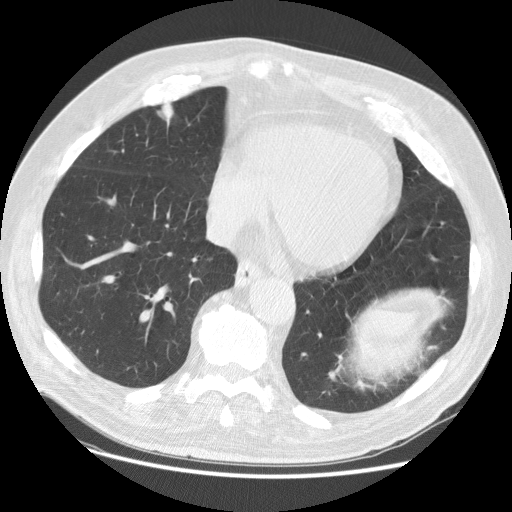
Low-dose screening chest CT, one axial slice. Position 38 of 129 along the scan axis. 140 kVp. Lung window (W 1500 / L -600 HU). 2.5 mm slice thickness. 512 × 512 image matrix, field of view 397 × 397 mm.
Structures marked on this image (expert manual segmentation):
- lesion 1 (tumor, upper lobe of right lung): bounding box <160,103,174,120> (left, top, right, bottom; pixels)